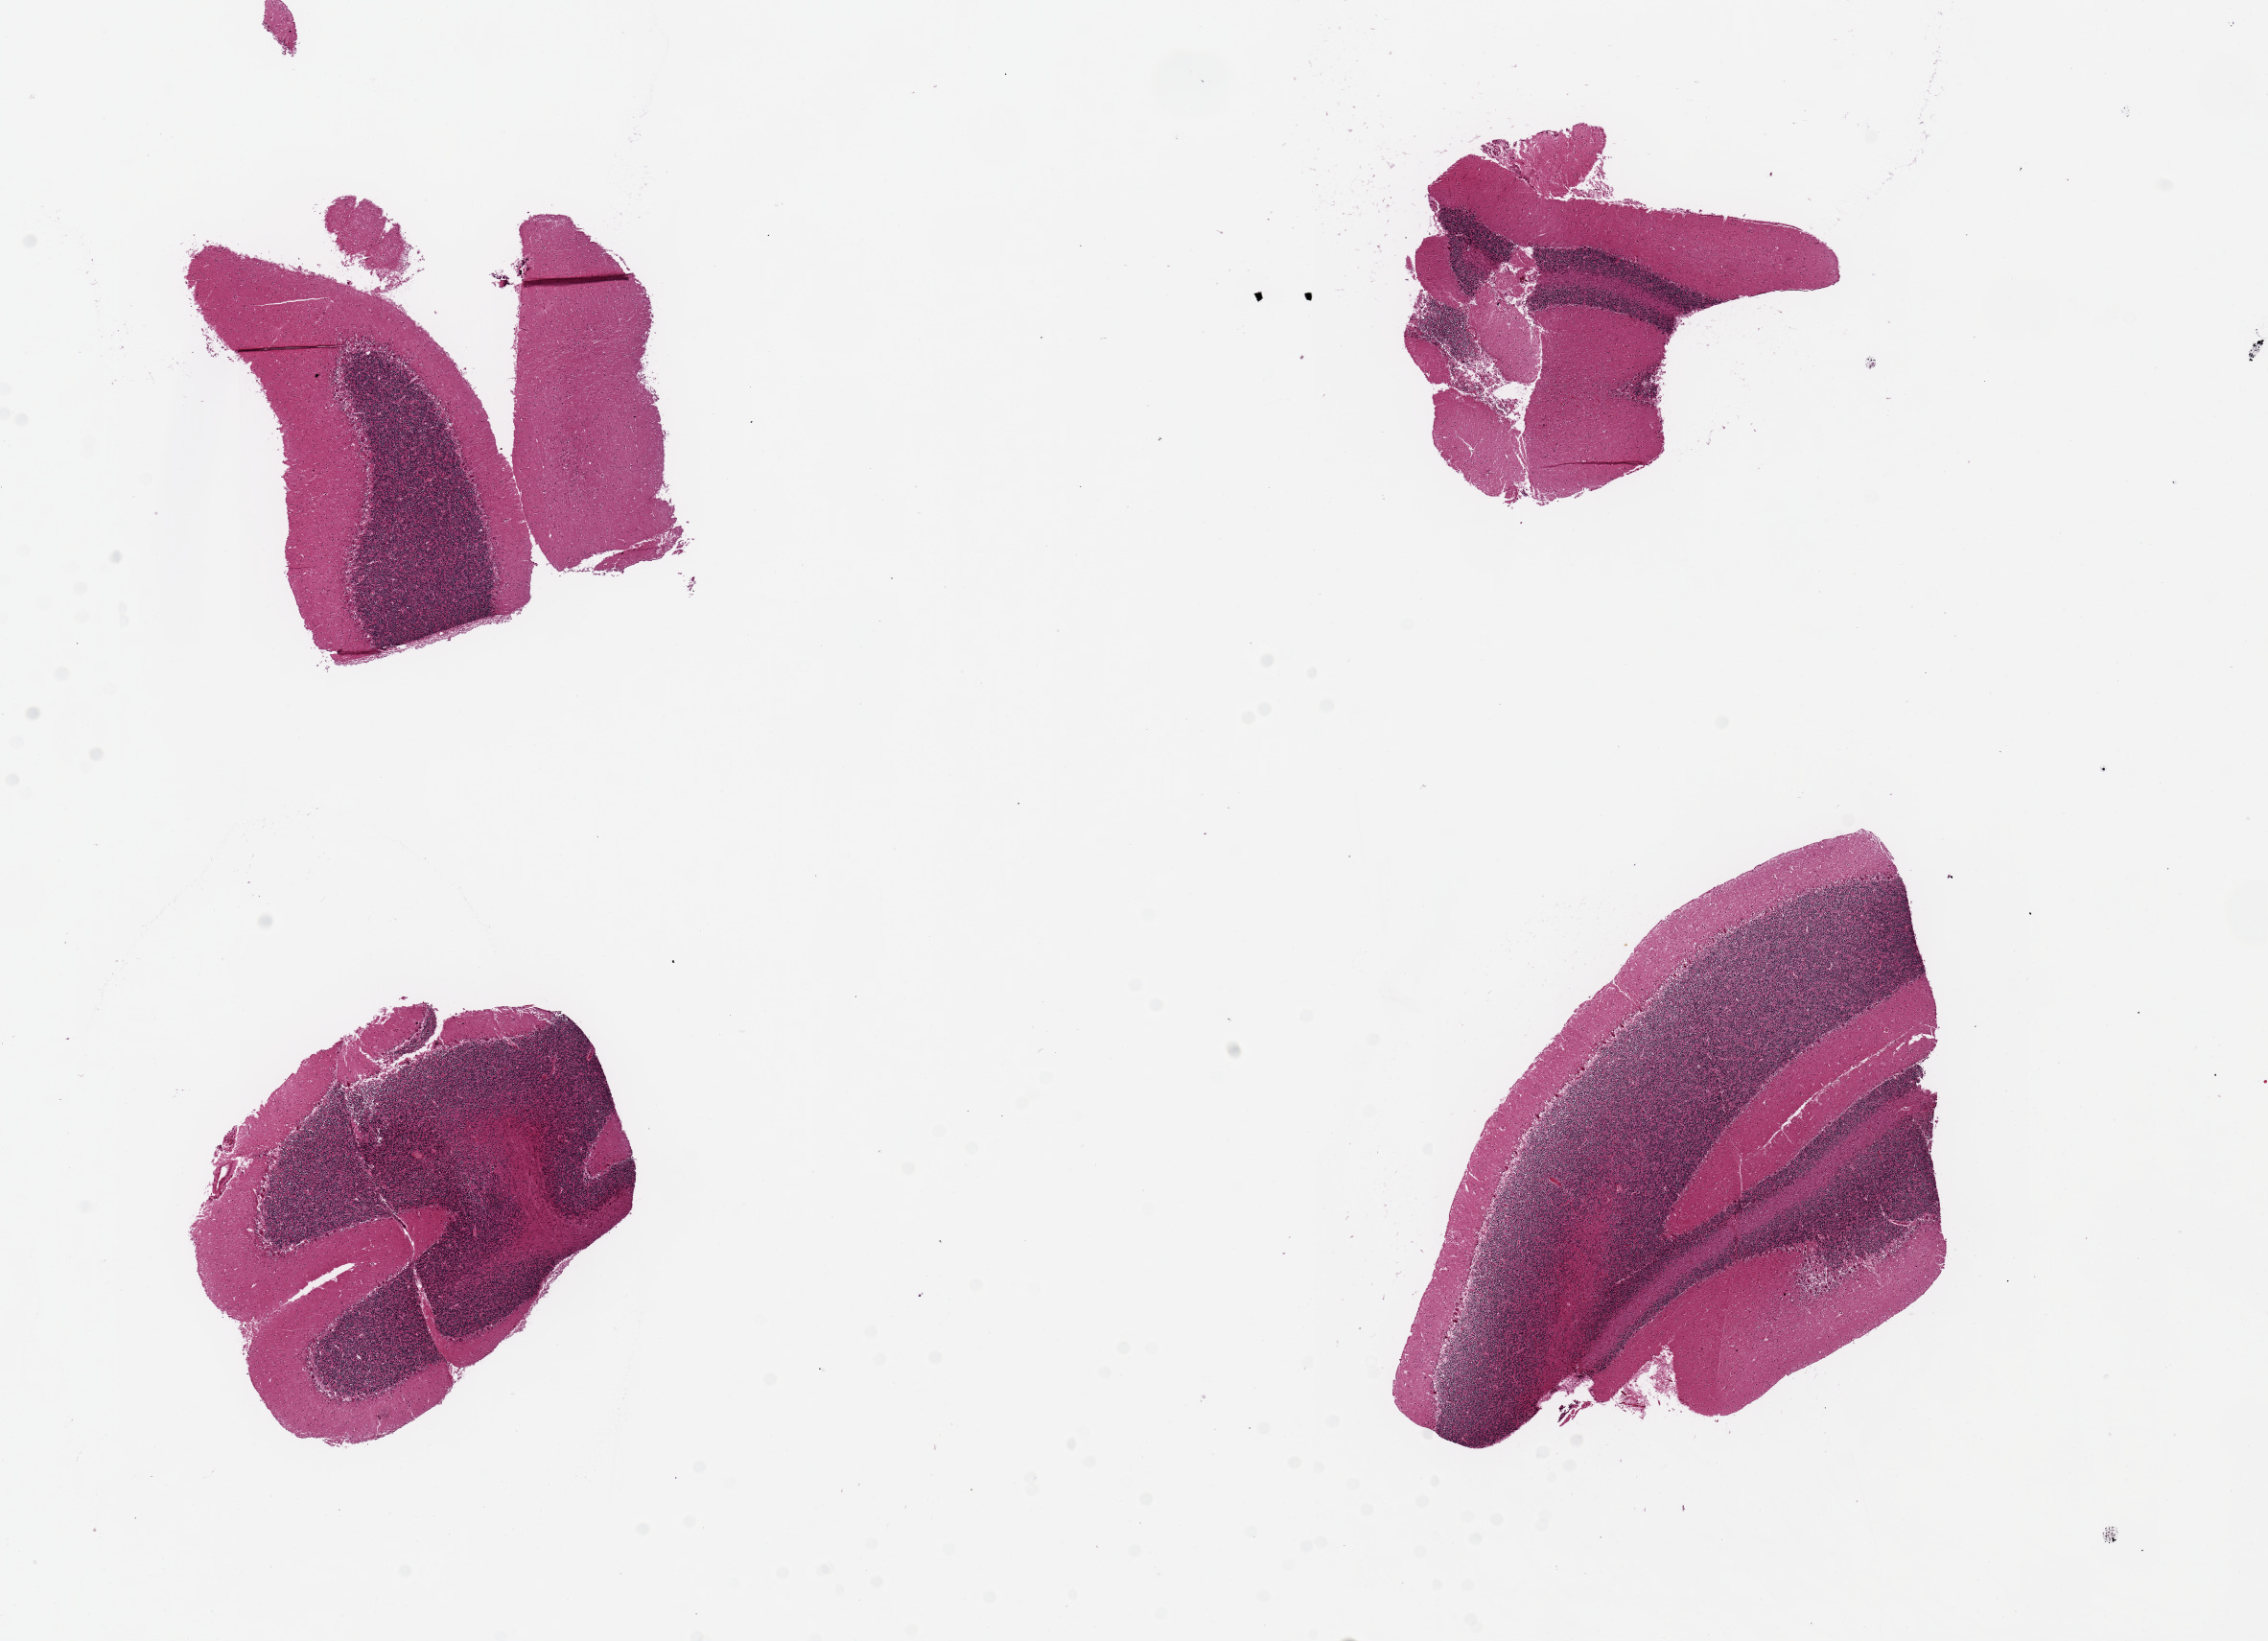
Haematoxylin and eosin whole-slide image, low-resolution overview of the scanned area, about 18.7 x 13.5 mm, PAXgene-fixed paraffin-embedded (PFPE) section, sampled site (target tissue): cerebellum, donor tissue sample. Donor: male.
Pathologist's review note for this sample: 4 pieces, up to 6x4mm.